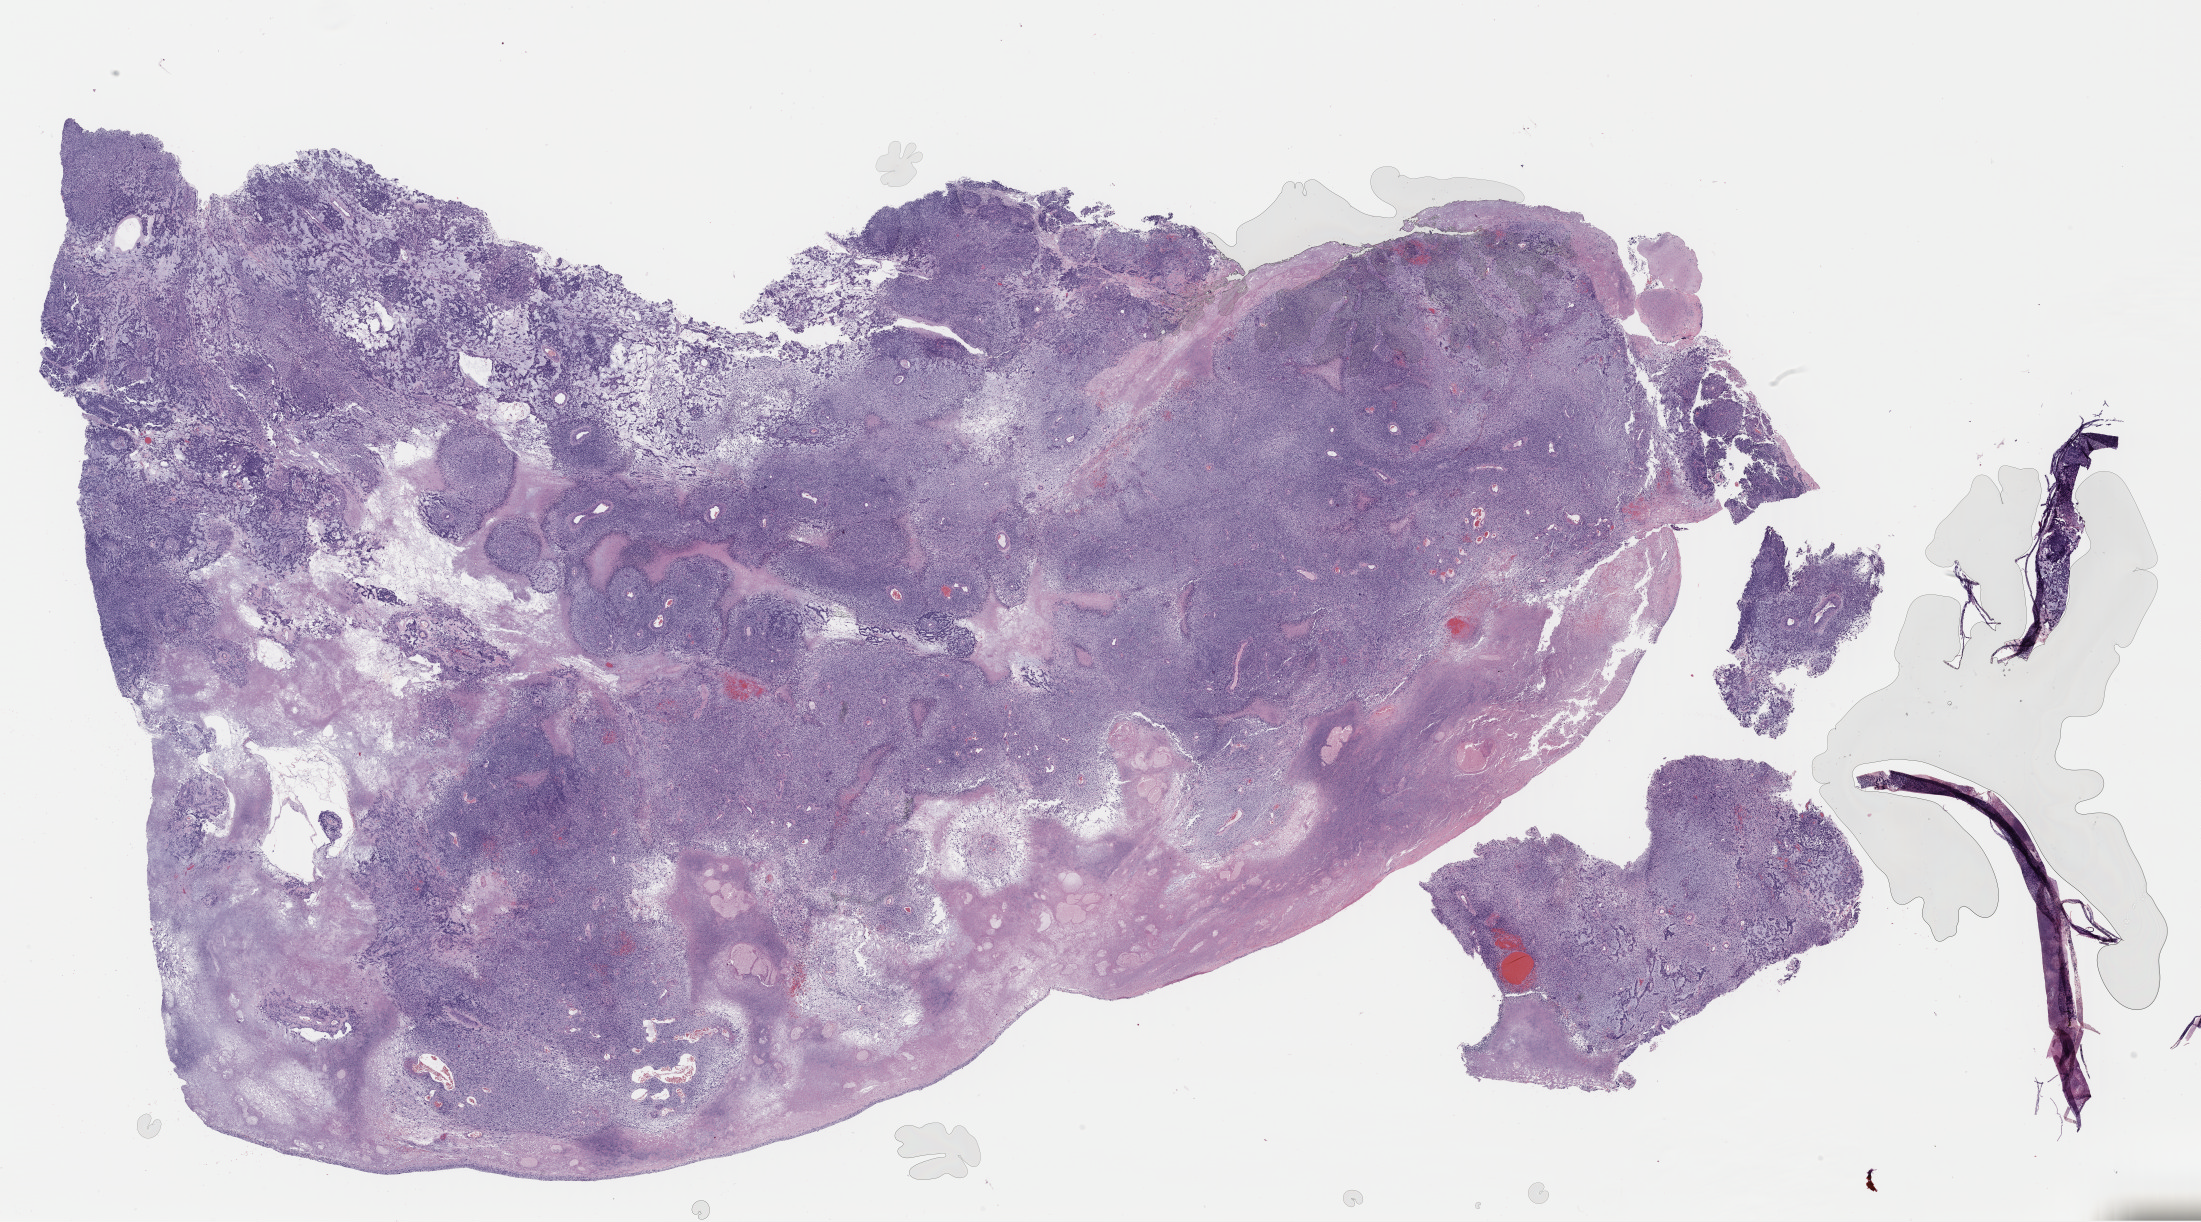
H&E-stained whole-slide image, a low-resolution overview of the entire scanned area, about 34.6 x 19.2 mm (from a 40x scan). Formalin-fixed paraffin-embedded (FFPE) diagnostic section. Primary tumour sample from the uterus. Patient: female, age at initial diagnosis 59 years.
Histologic diagnosis: Mullerian mixed tumor (endometrium). FIGO stage: IA.